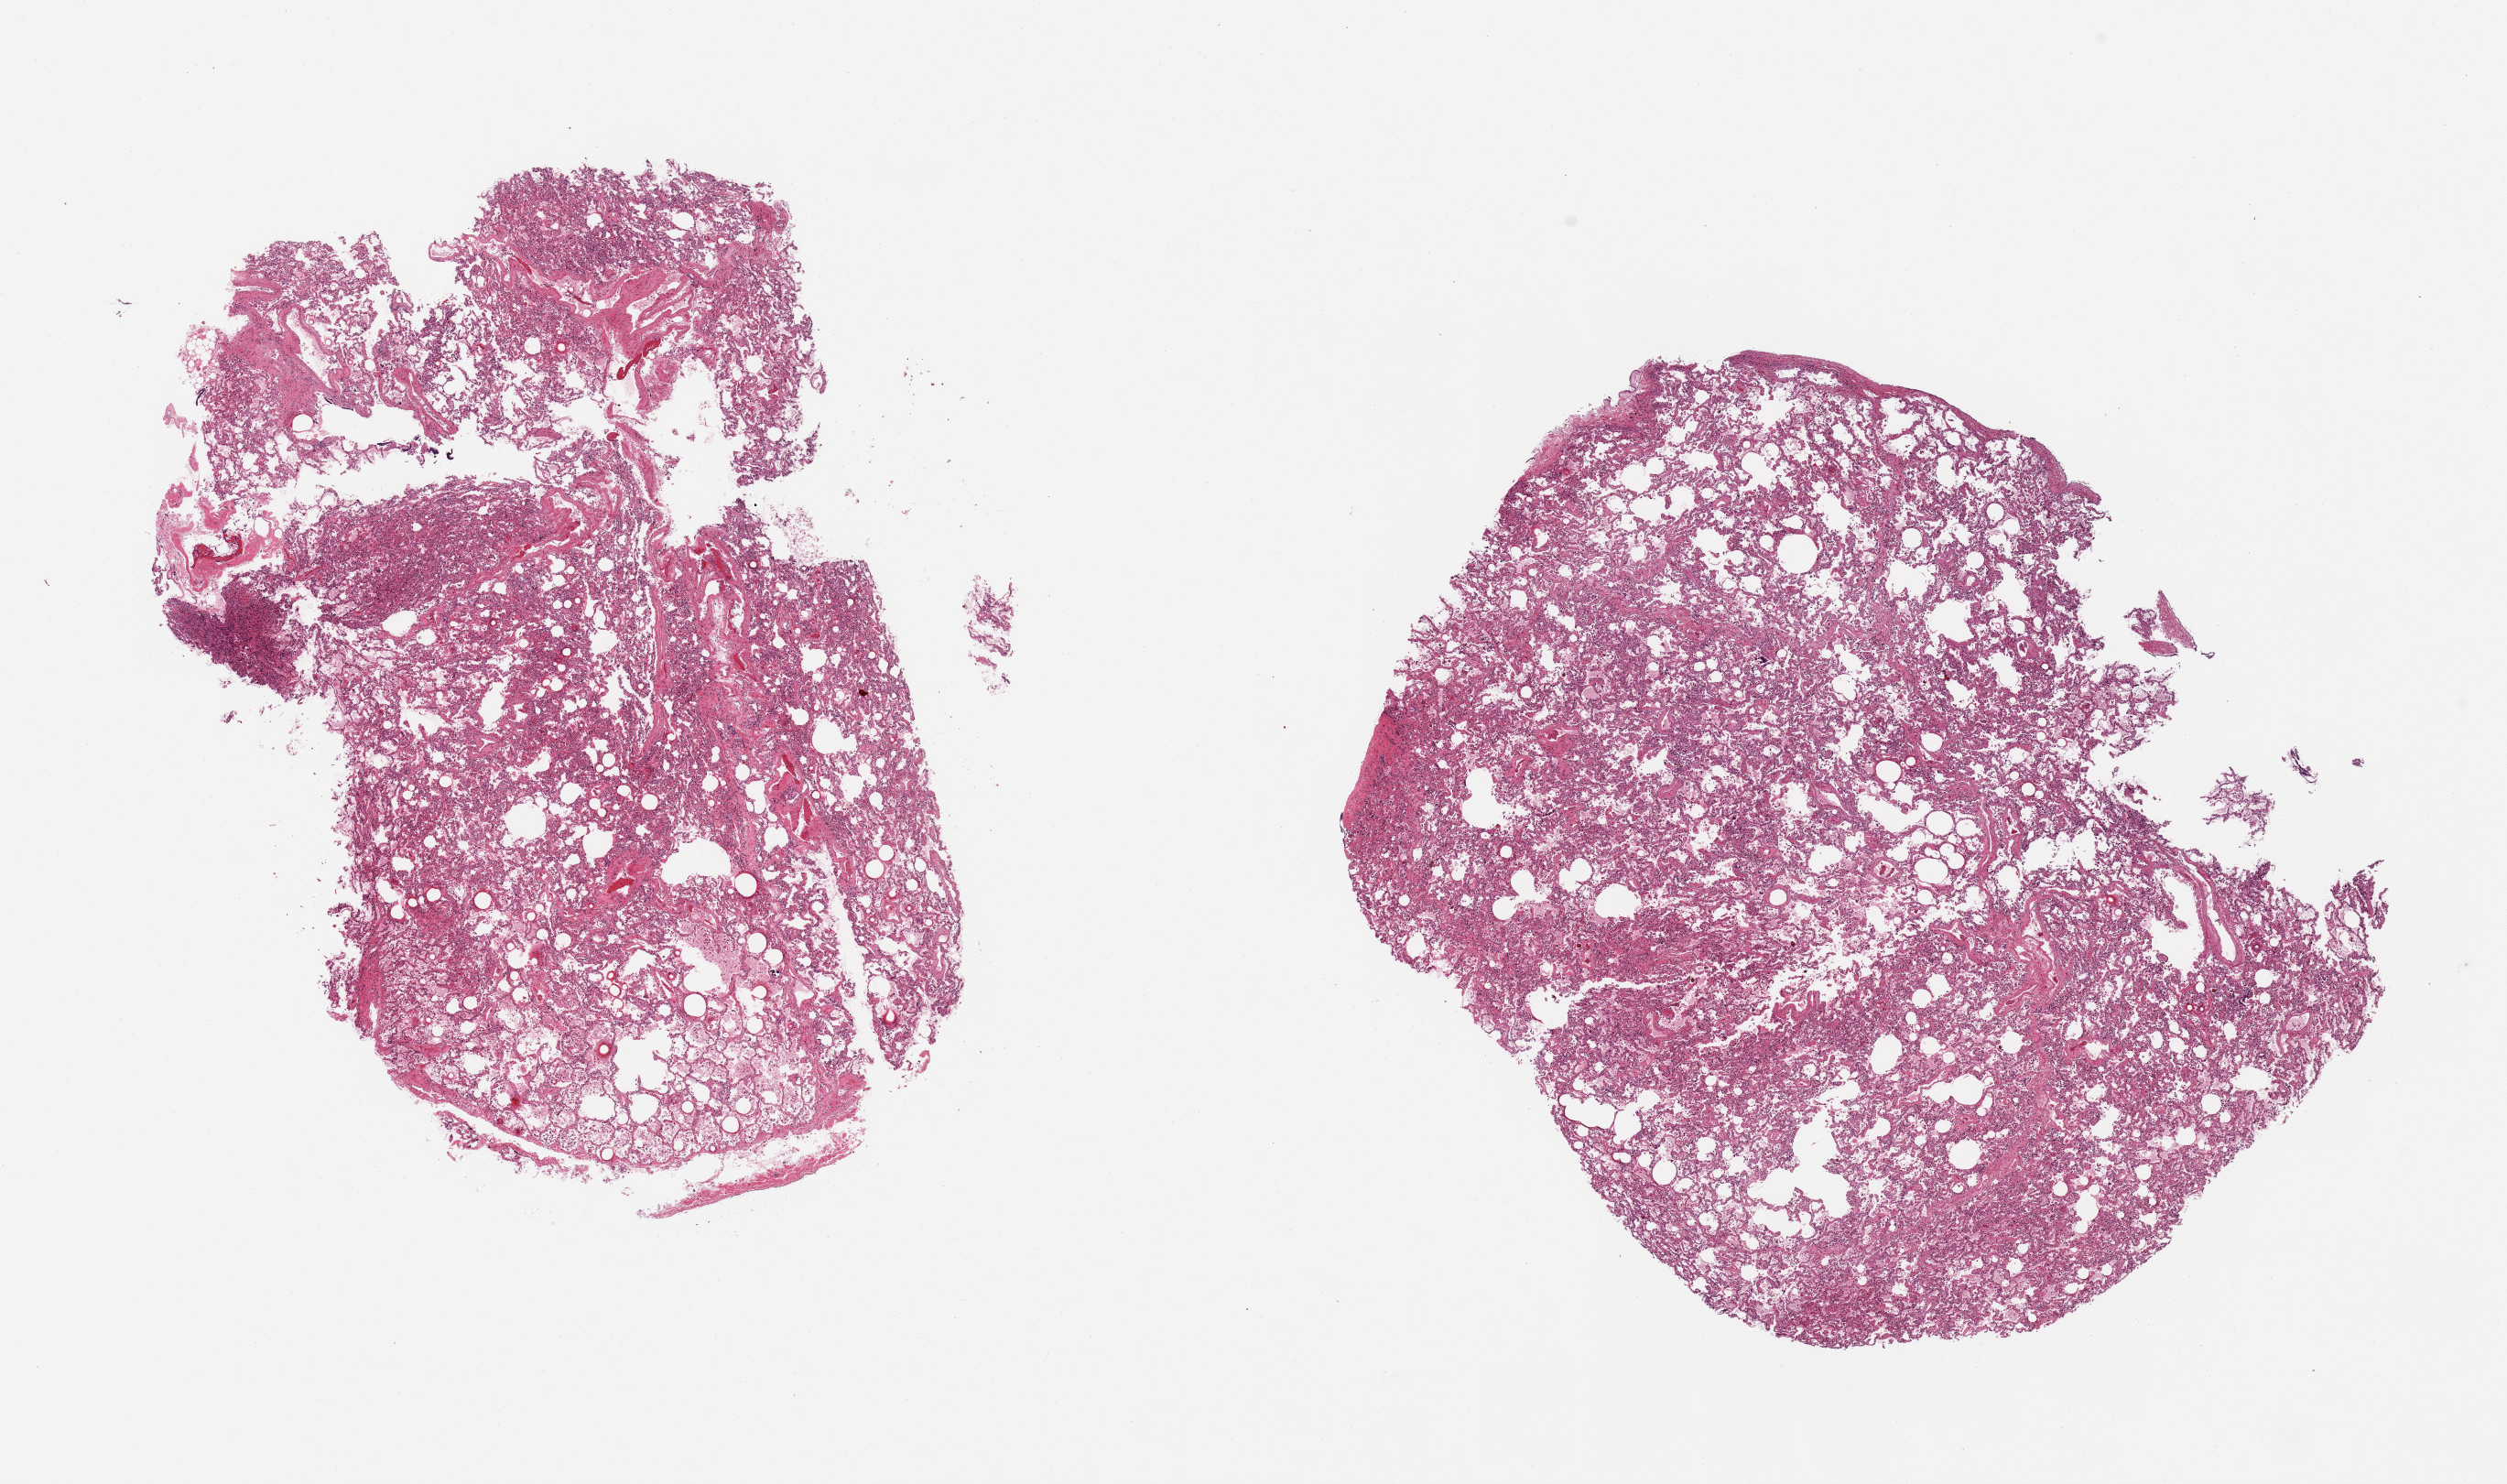
Digitized H&E-stained section, brightfield, whole scanned area (about 21.7 x 12.8 mm) shown as a low-resolution overview. PAXgene-fixed, paraffin-embedded tissue. Section of lung (target tissue). Donor tissue sample. Donor: male.
• review note (as recorded): 2 pieces